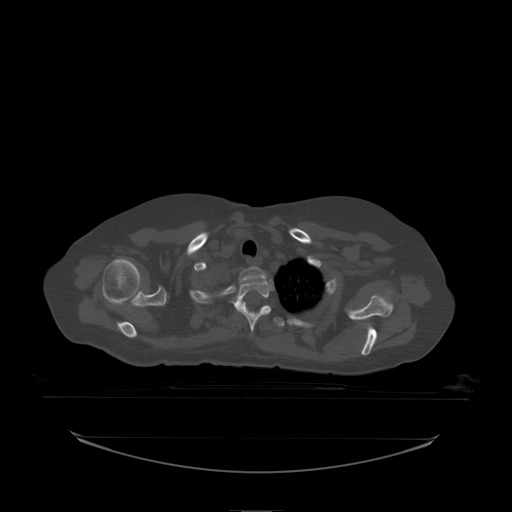
CT including the spine, one axial slice. Bone window (W 1800 / L 400 HU). 2.5 mm slice thickness. 512 × 512 image matrix, field of view 500 × 500 mm. Female patient, age 53 years. From the clinical record (not read from this slice): primary cancer: lung; vertebrae with lytic lesions (as recorded): T7, L1.
Annotated regions visible in this slice (semi-automatically segmented with operator editing):
- T1 vertebra: bounding box <239,267,267,283> (left, top, right, bottom; pixels)
- T2 vertebra: <232,278,272,333>
- T3 vertebra: <264,306,285,327>